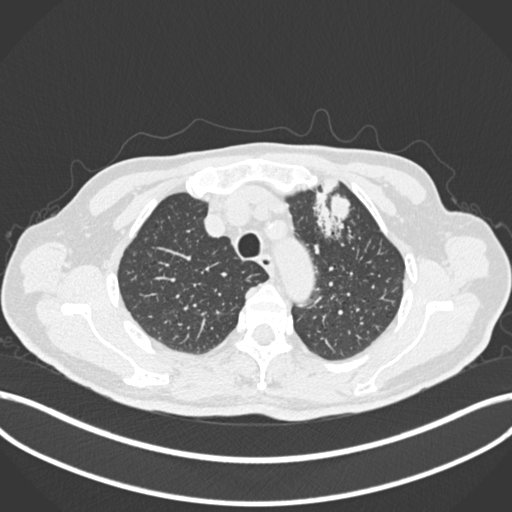
Chest CT, one axial slice; position 206 of 261 along the scan axis; reconstruction kernel B30f; lung window (W 1500 / L -600 HU); 1 mm slice thickness; 512 × 512 image matrix, field of view 400 × 400 mm. Patient: male, 74 years. Case-level facts recorded for this patient, not image findings: clinical TNM (as recorded): T2b N0 M1c.
Outlined on this slice (bounding box drawn by a radiologist):
- lung tumour (recorded histology: adenocarcinoma): box from (x=307, y=177) to (x=355, y=241) px